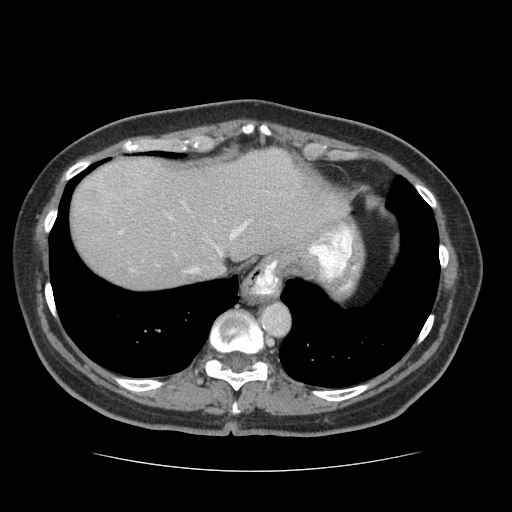
Contrast-enhanced abdominal CT (liver protocol), one axial slice; position 60 of 75 along the scan axis; reconstruction kernel STANDARD; soft-tissue window (W 400 / L 40 HU); 512 × 512 image matrix. Case-level facts recorded for this patient, not image findings: diagnosis: hepatocellular carcinoma (patient treated with transarterial chemoembolisation; whether this scan precedes or follows treatment is not stated here); TNM stage (as recorded): Stage-I; Child-Pugh class: A; tumour differentiation: moderately differentiated; tumour nodularity: uninodular.
Outlined on this slice (semi-automatically segmented with operator editing):
- abdominal aorta: bounding box (x1, y1, x2, y2) in pixels: (262, 303, 290, 334)
- liver parenchyma outside the tumour (the mass and vessels are separate outlines, so this box may not span the whole liver): (70, 148, 348, 288)
- liver vessels: (97, 183, 281, 273)